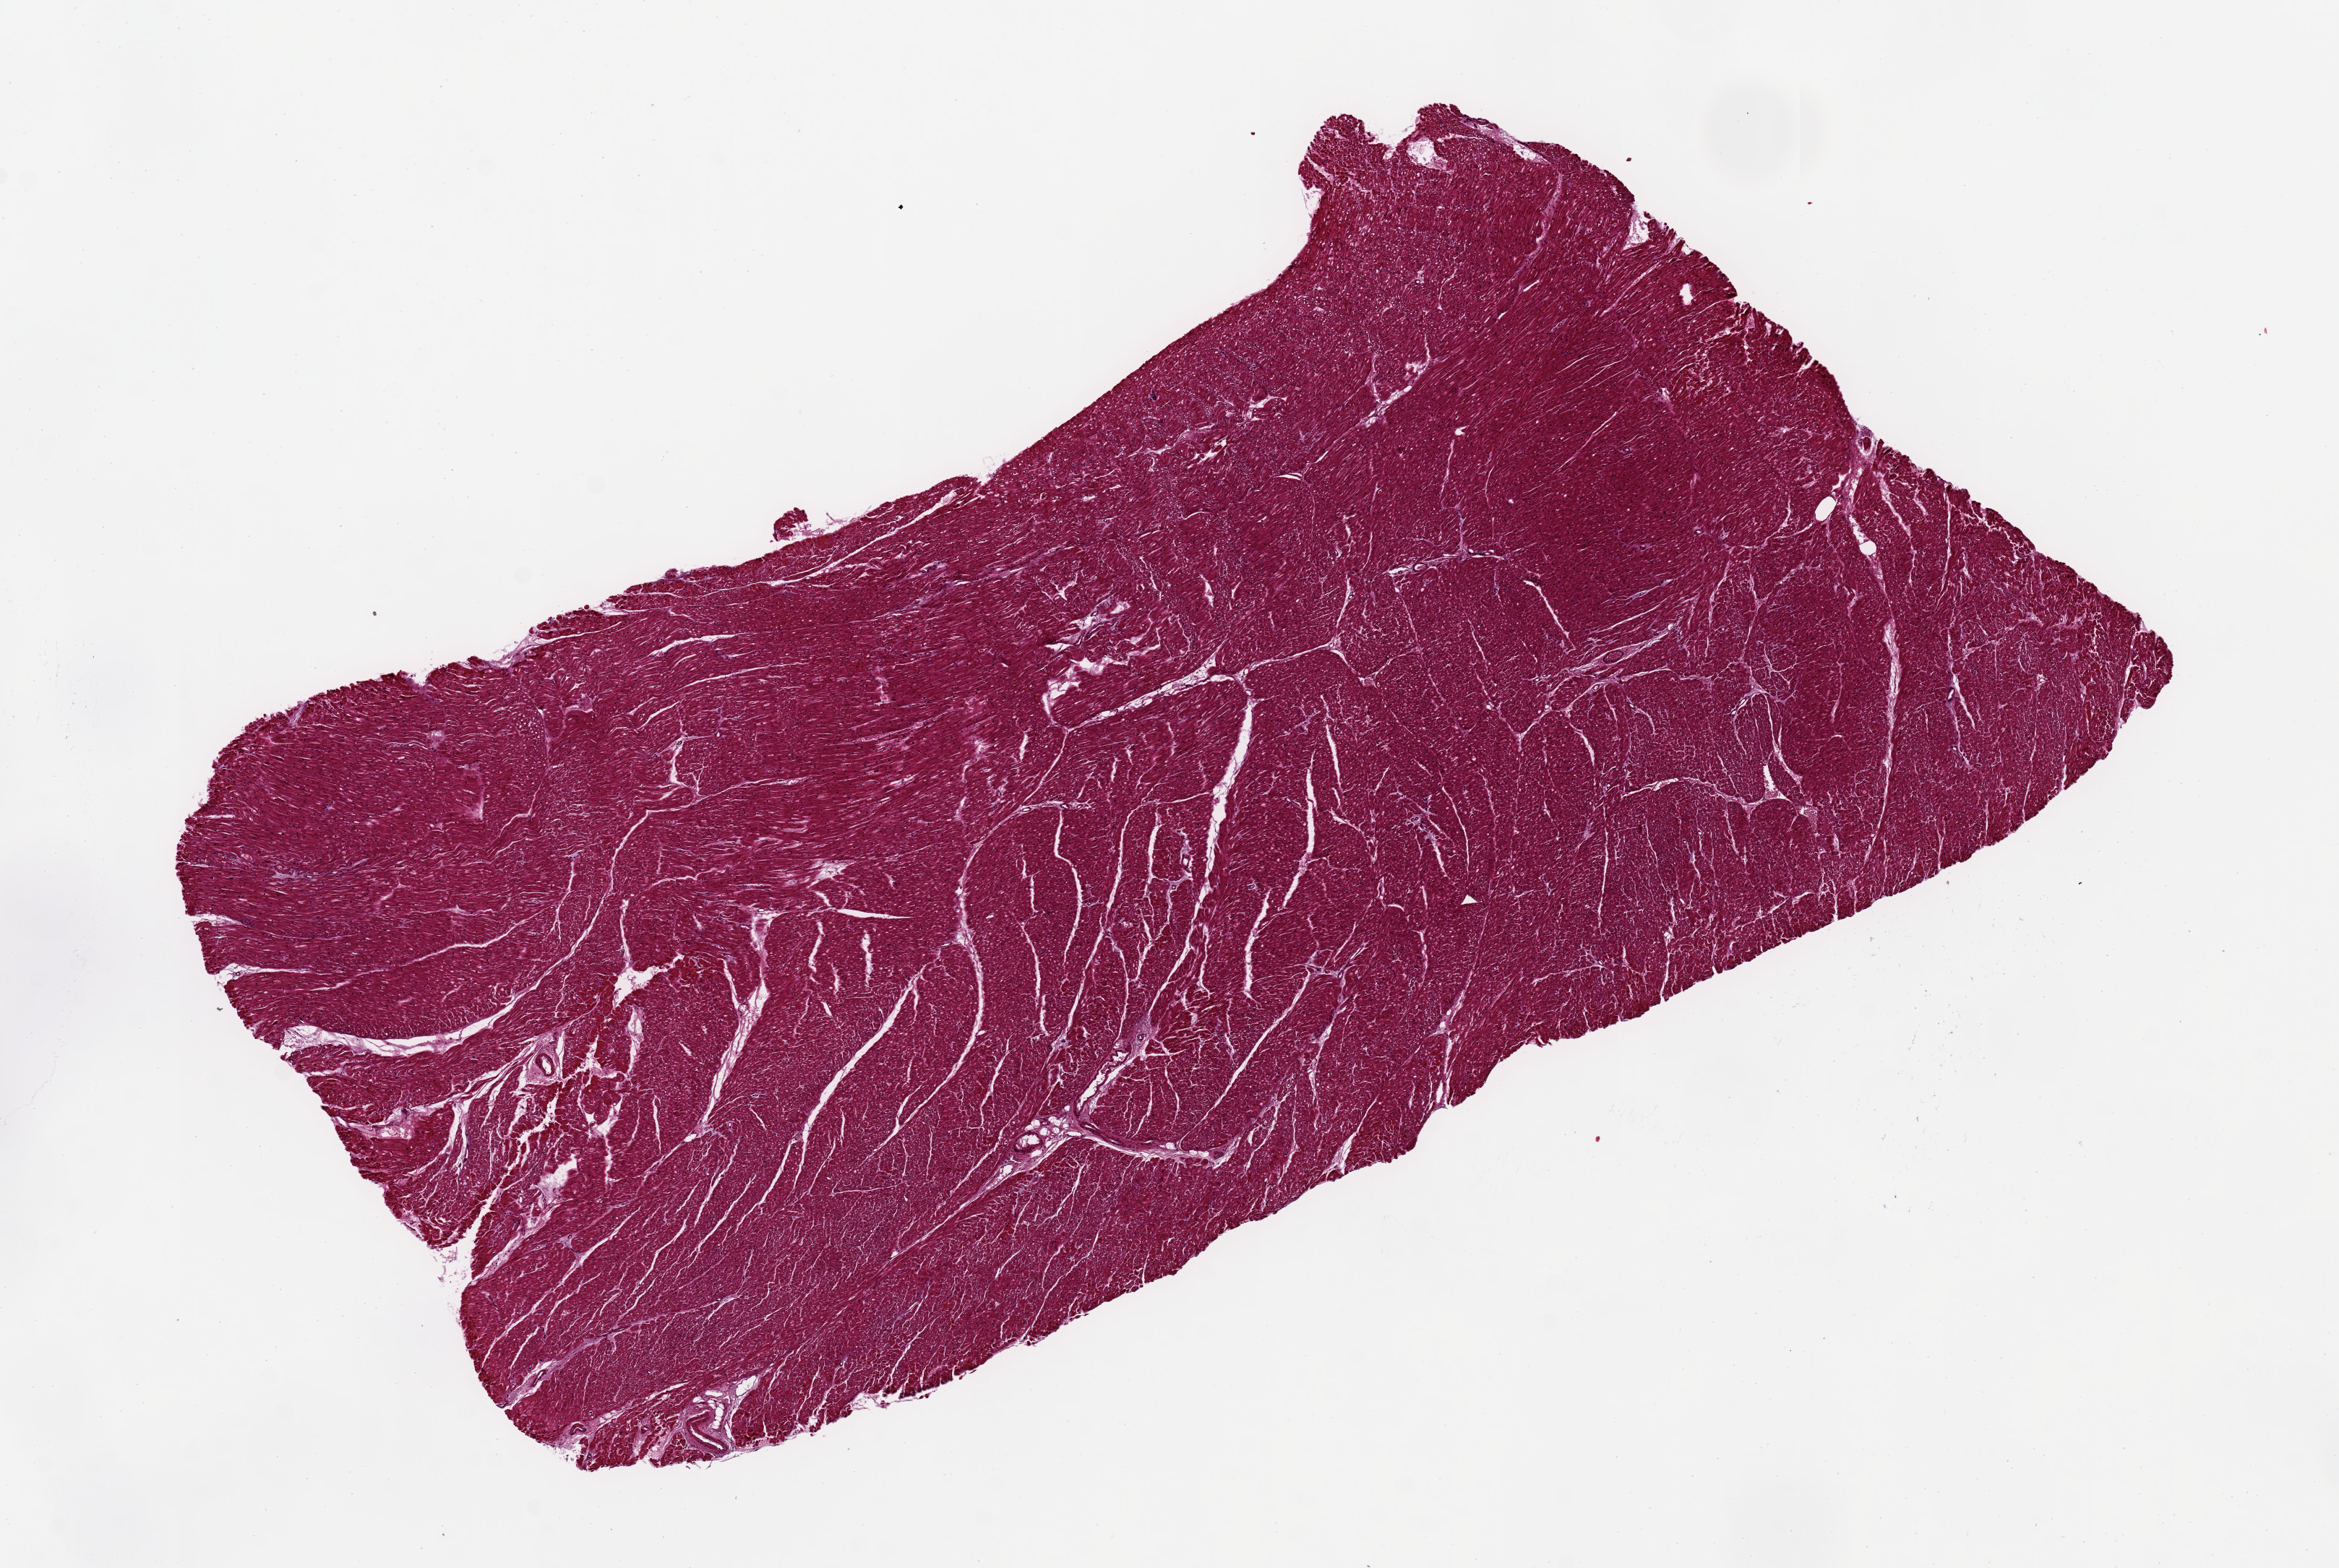
Whole-slide image, haematoxylin and eosin stain, brightfield, low-resolution overview of the scanned area, about 12.8 x 8.6 mm; PAXgene-fixed, paraffin-embedded tissue; sampled site (target tissue): heart; donor tissue sample.
Pathologist's review note for this sample: 8x4.5mm. Contraction bands and nuclear hypertrophy c/w ischemic damage.